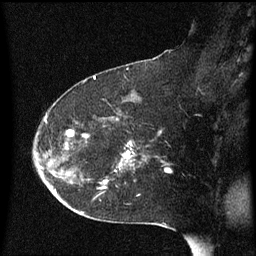
Breast MRI (dynamic contrast-enhanced), one sagittal slice; slice 36 of 60 in the series (ordered by position); dynamic contrast-enhanced series, image 2 of 3 at this slice position (ordered by acquisition); 1.5 T; TE 4.2 ms, TR 8.4 ms; 2 mm slice thickness; 256 × 256 image matrix. Patient: female, 54 years. From the clinical record (not read from this slice): setting: breast cancer imaged before/during neoadjuvant chemotherapy; receptor status: HR-positive, HER2-negative.
Structures marked on this image (semi-automatically segmented with operator editing):
- analysis volume of interest (the breast-tissue region the enhancement analysis was run in; not a lesion): bounding box <102,120,170,185> (left, top, right, bottom; pixels)
- tumour enhancement mask (voxels above the 70 % enhancement threshold inside the analysis volume of interest): <104,152,131,185>